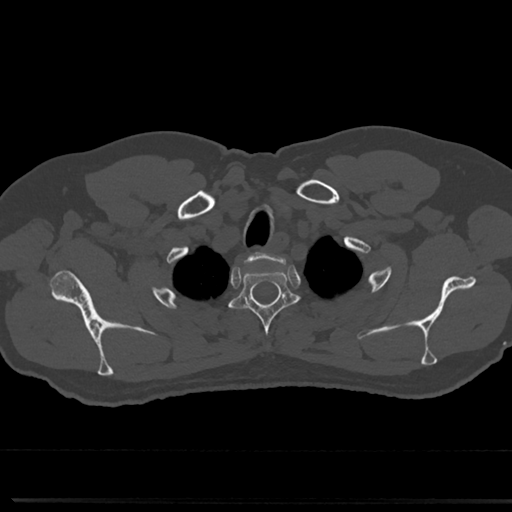
CT including the spine, one axial slice; slice 637 of 817 in the series (ordered by position); reconstruction kernel Br40s/3; bone window (W 1800 / L 400 HU); 0.5 mm slice thickness; 512 × 512 image matrix. Patient: male, 61 years. From the clinical record (not read from this slice): primary cancer: prostate.
Outlined on this slice (semi-automatically segmented with operator editing):
- T2 vertebra: bounding box (x1, y1, x2, y2) in pixels: (233, 262, 295, 354)
- T3 vertebra: (302, 313, 310, 322)